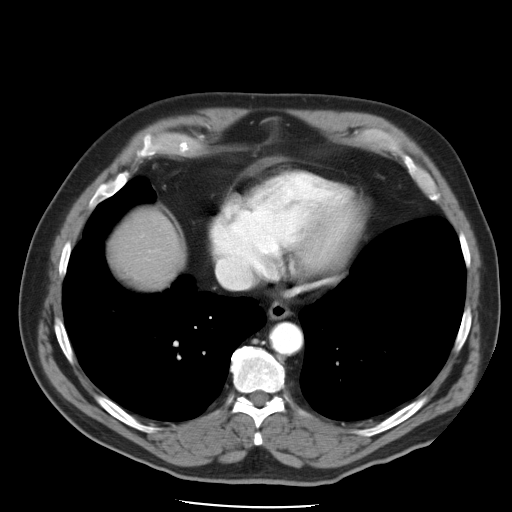
Contrast-enhanced abdominal CT, one axial slice; slice 45 of 49 in the series (ordered by position); intravenous contrast given; soft-tissue window (W 400 / L 40 HU); 512 × 512 image matrix. Male patient, age 68 years. From the clinical record (not read from this slice): diagnosis: colorectal cancer liver metastases, imaged before liver resection; multiple liver metastases: yes; largest metastasis: 1.7 cm; chemotherapy before resection: yes.
Annotated regions visible in this slice (outlined manually by an expert reader):
- hepatic veins: bounding box [x1, y1, x2, y2] px = [216, 253, 254, 289]
- liver: [115, 214, 182, 279]
- planned liver remnant (the part of the liver to remain after resection): [116, 214, 182, 279]